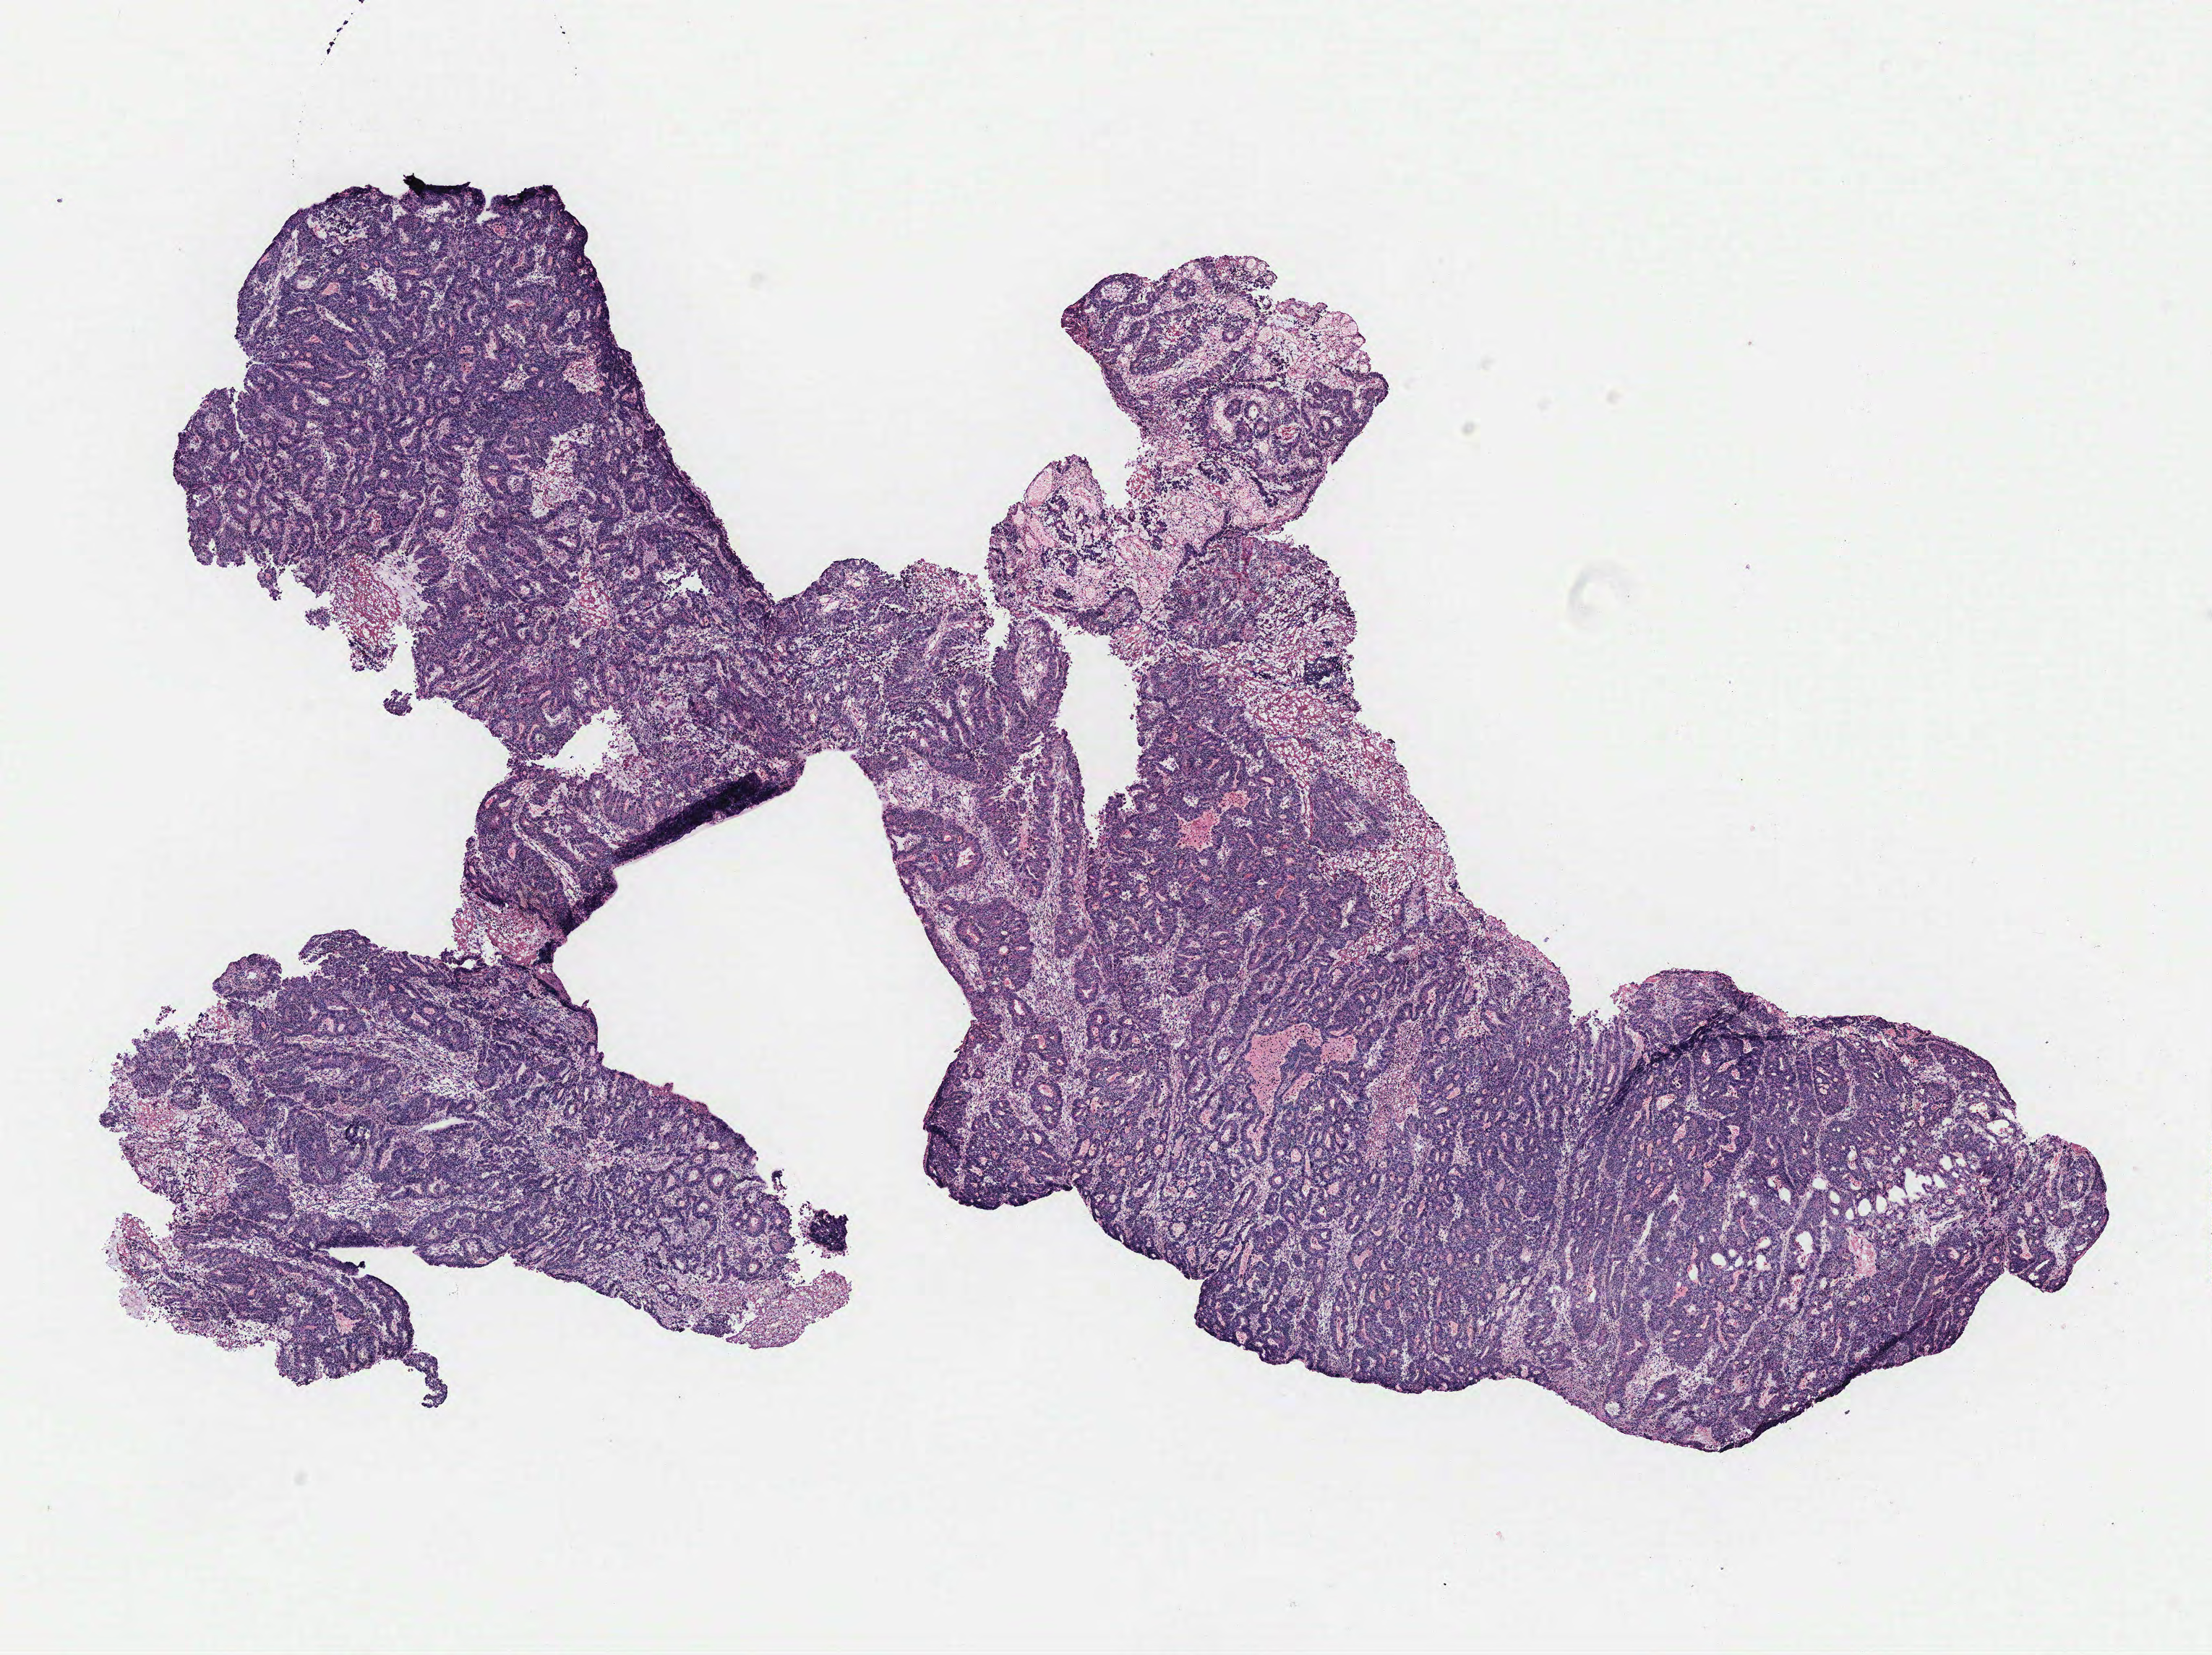
Hematoxylin and eosin (H&E) stained whole-slide image — a low-resolution overview of the entire scanned area, about 12.2 x 9.2 mm, colon, tumour tissue. 49-year-old female patient.
- primary tumour site (as recorded): colon
- patient diagnosis (cohort enrolment): colon cancer (colon)